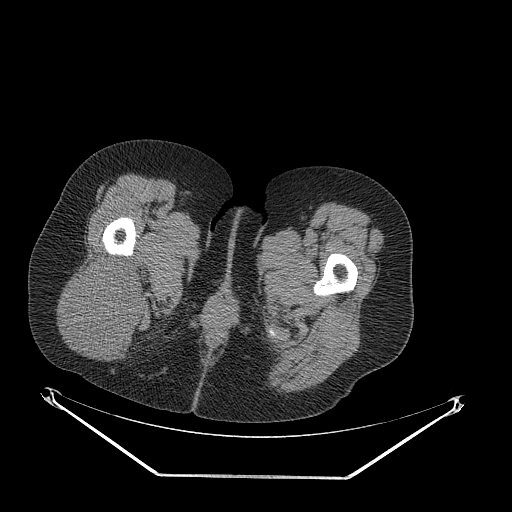
CT of an extremity soft-tissue mass (from a PET/CT study), one axial slice. Slice 50 of 257 in the series (ordered by position). Reconstruction kernel STANDARD. 140 kVp. Soft-tissue window (W 400 / L 40 HU). 3.75 mm slice thickness. 512 × 512 image matrix, field of view 500 × 500 mm. Female patient. From the clinical record (not read from this slice): histological type: synovial sarcoma; grade: intermediate; site of the primary tumour: right buttock.
Outlined on this slice (expert contour drawn on MRI and transferred to this co-registered scan by the dataset authors):
- gross tumour volume including surrounding oedema: bounding box (x1, y1, x2, y2) in pixels: (68, 256, 147, 350)
- gross tumour volume (mass): (68, 256, 147, 350)